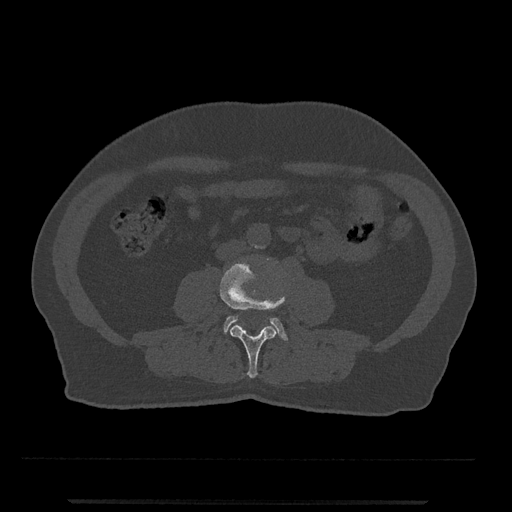
CT including the spine, one axial slice; slice 180 of 797 in the series (ordered by position); bone window (W 1800 / L 400 HU); 0.5 mm slice thickness; 512 × 512 image matrix, field of view 419 × 419 mm. Male patient, age 63 years. From the clinical record (not read from this slice): primary cancer: prostate.
Structures marked on this image (semi-automatically segmented with operator editing):
- L3 vertebra: bounding box [x1, y1, x2, y2] px = [220, 261, 286, 379]
- L4 vertebra: [224, 316, 287, 340]